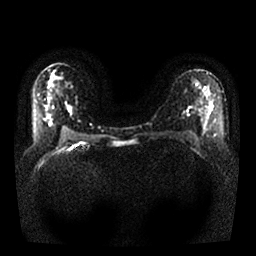
Breast MRI, one axial slice. Diffusion-weighted series; image 2 of 4 stored at this slice position (different b-values; order by instance number). 1.5 T. 4 mm slice thickness. 256 × 256 image matrix. Female patient.
Outlined on this slice (expert manual segmentation):
- tumour on diffusion-weighted imaging: bounding box (x1, y1, x2, y2) in pixels: (206, 104, 212, 115)